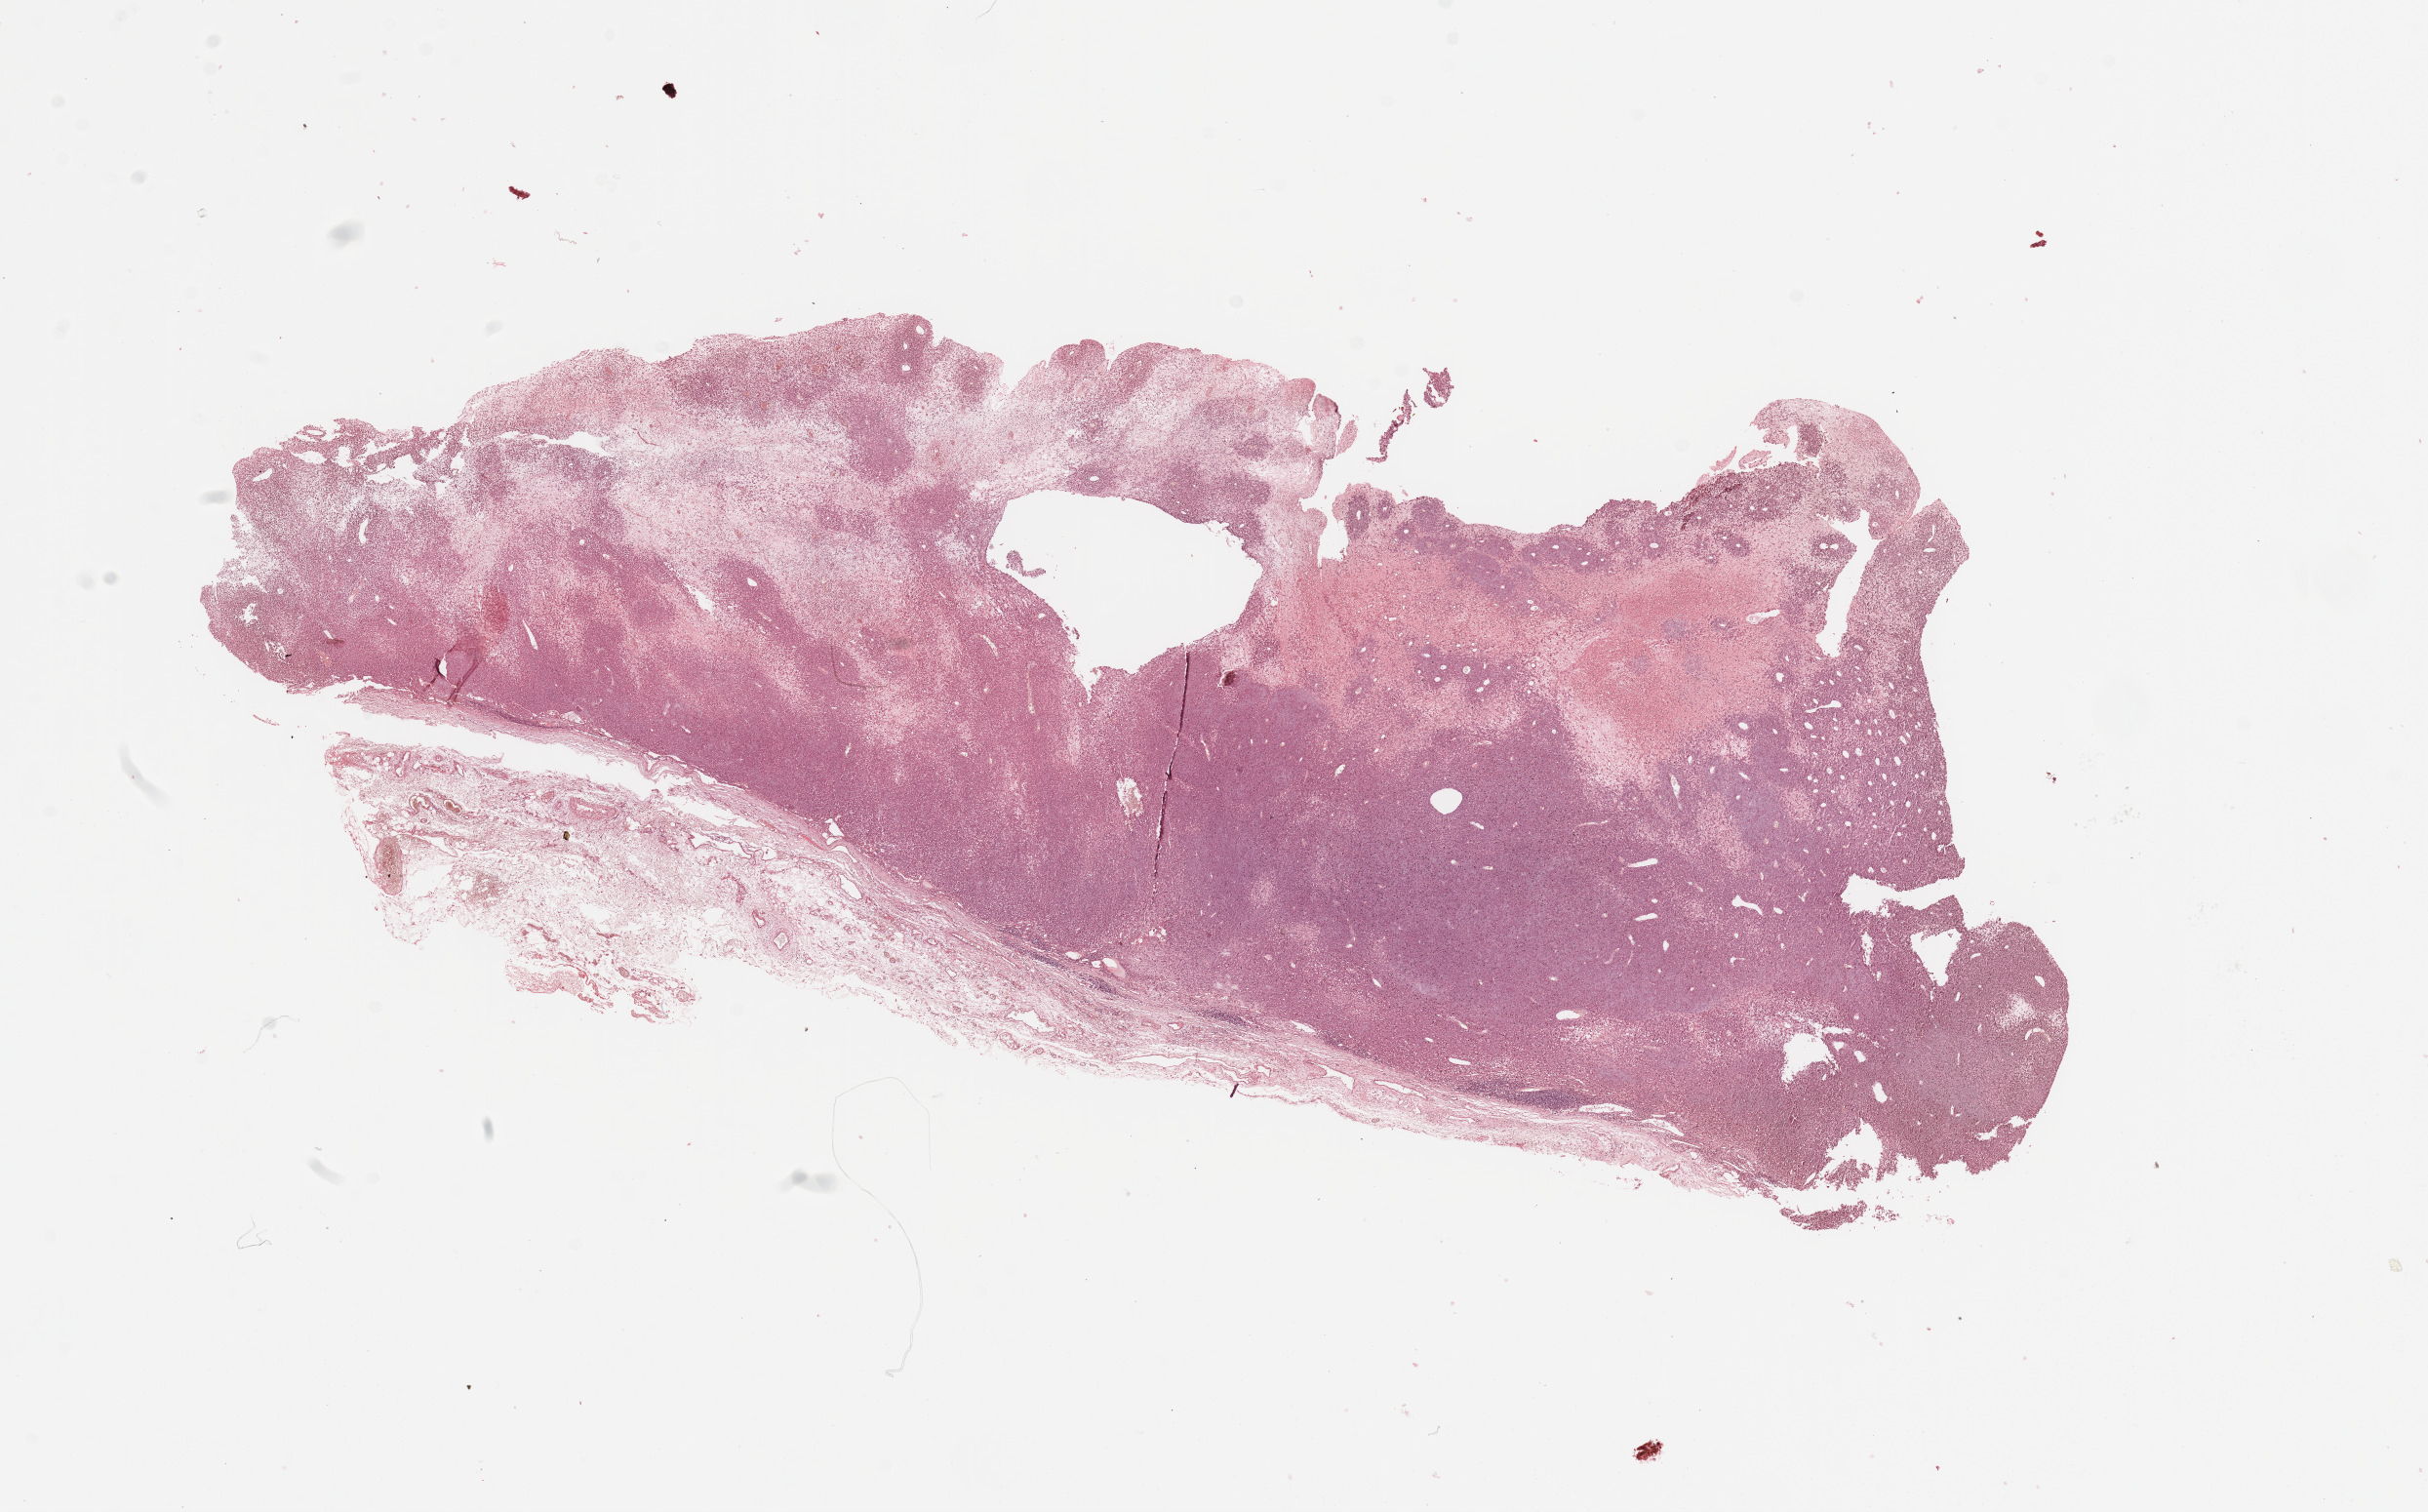
Whole-slide histology image, Hematoxylin and eosin (H&E) stained, whole scanned area (about 19.7 x 12.3 mm, slide scanned at 20x) shown as a low-resolution overview, melanoma tumour tissue; sampled site not recorded. Female, 76 y/o.
AJCC pathologic stage: IB. Diagnosis: Malignant melanoma, NOS. Primary tumour site (as recorded): trunk.